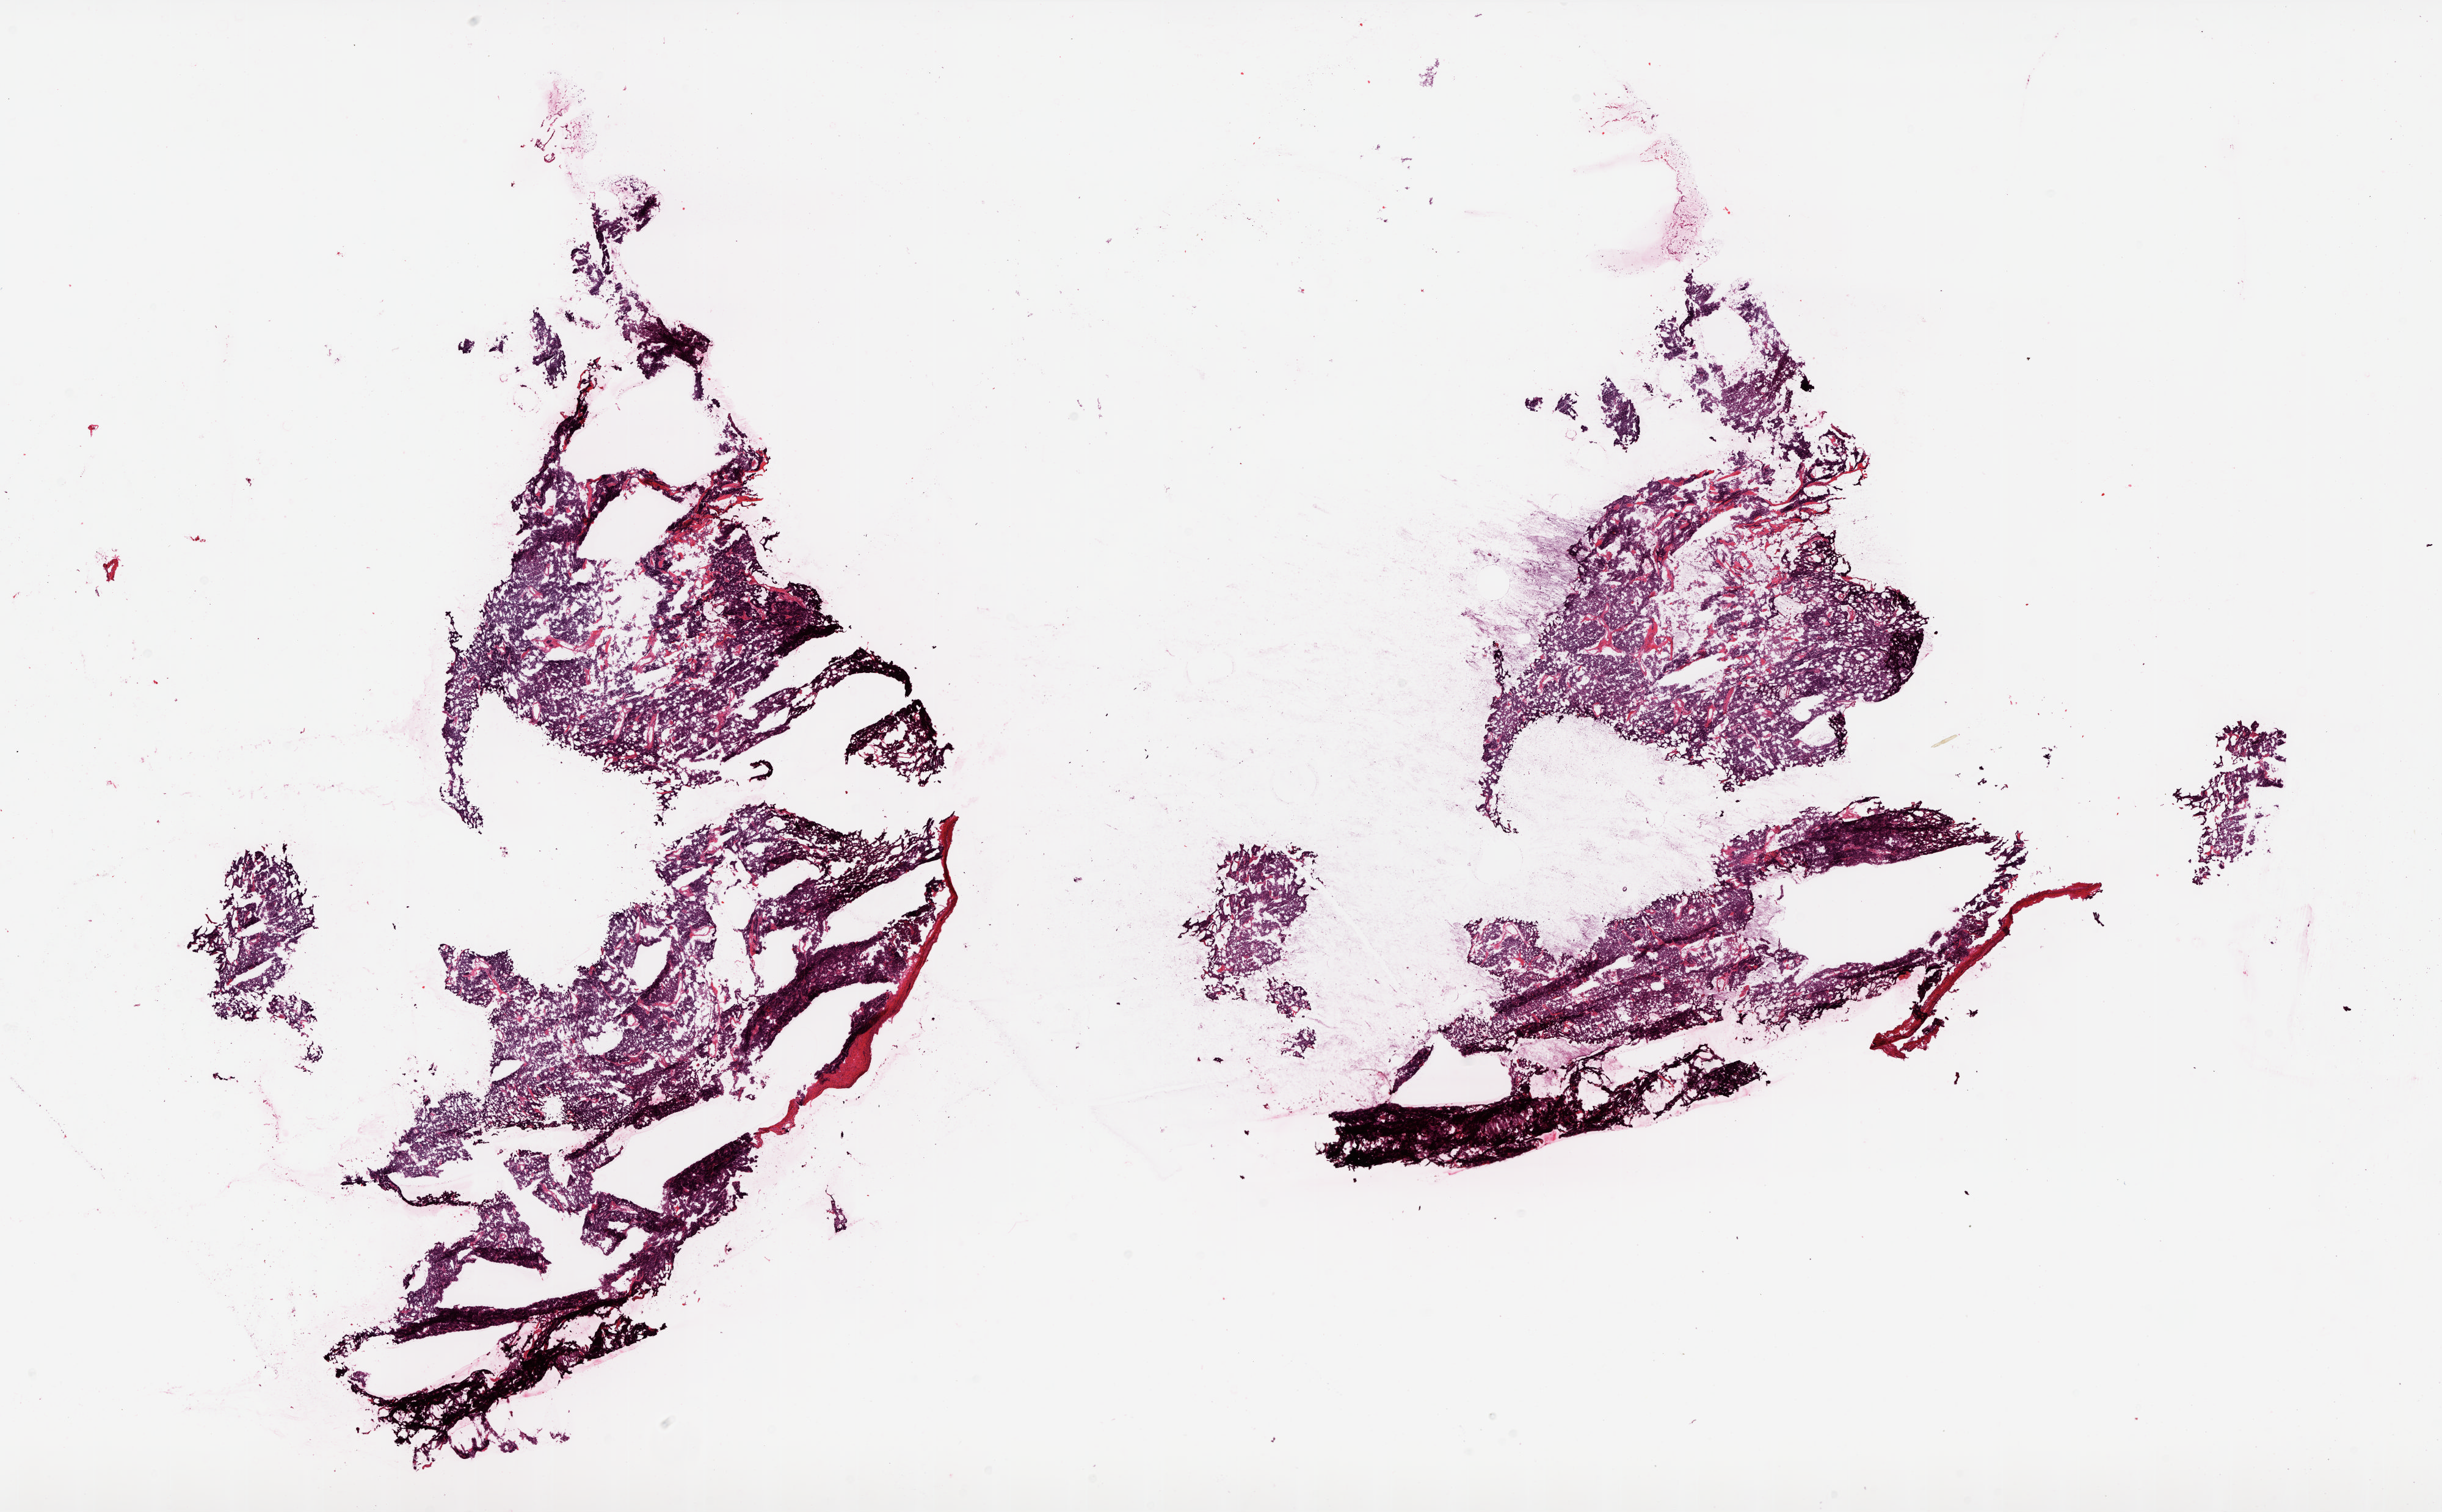
Hematoxylin and eosin (H&E) stained whole-slide image, a low-resolution overview of the entire scanned area, about 31.9 x 19.8 mm (slide scanned at 20x). Frozen section from the top of the tissue portion. Sample: primary tumour, ovary. Female, age 55 years at initial diagnosis. Histologic grade: G3 (poorly differentiated). Pathologist review of this section (percent, as recorded): tumour cells 92%, tumour nuclei 95%, normal cells 0%, stromal cells 4%, necrosis 4%.
Laterality: bilateral. Pathologic diagnosis: Serous cystadenocarcinoma, NOS. FIGO stage: IIIB.